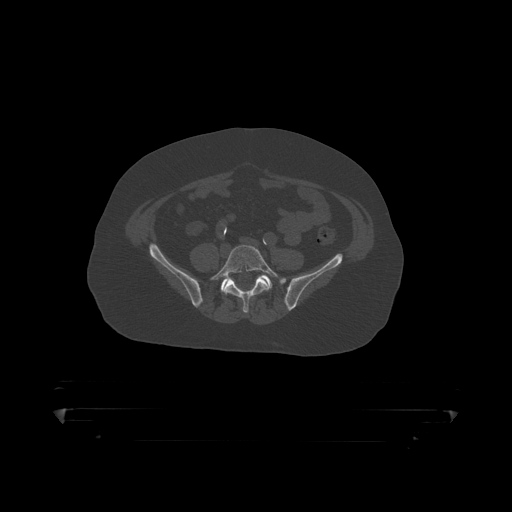
CT including the spine, one axial slice. Slice 38 of 390 in the series (ordered by position). Reconstruction kernel STANDARD. Bone window (W 1800 / L 400 HU). 512 × 512 image matrix, field of view 650 × 650 mm. Male patient, age 60 years. From the clinical record (not read from this slice): primary cancer: prostate.
Annotated regions visible in this slice (semi-automatic segmentation, software-assisted and operator-edited):
- L5 vertebra: bounding box [x1, y1, x2, y2] px = [209, 244, 281, 314]